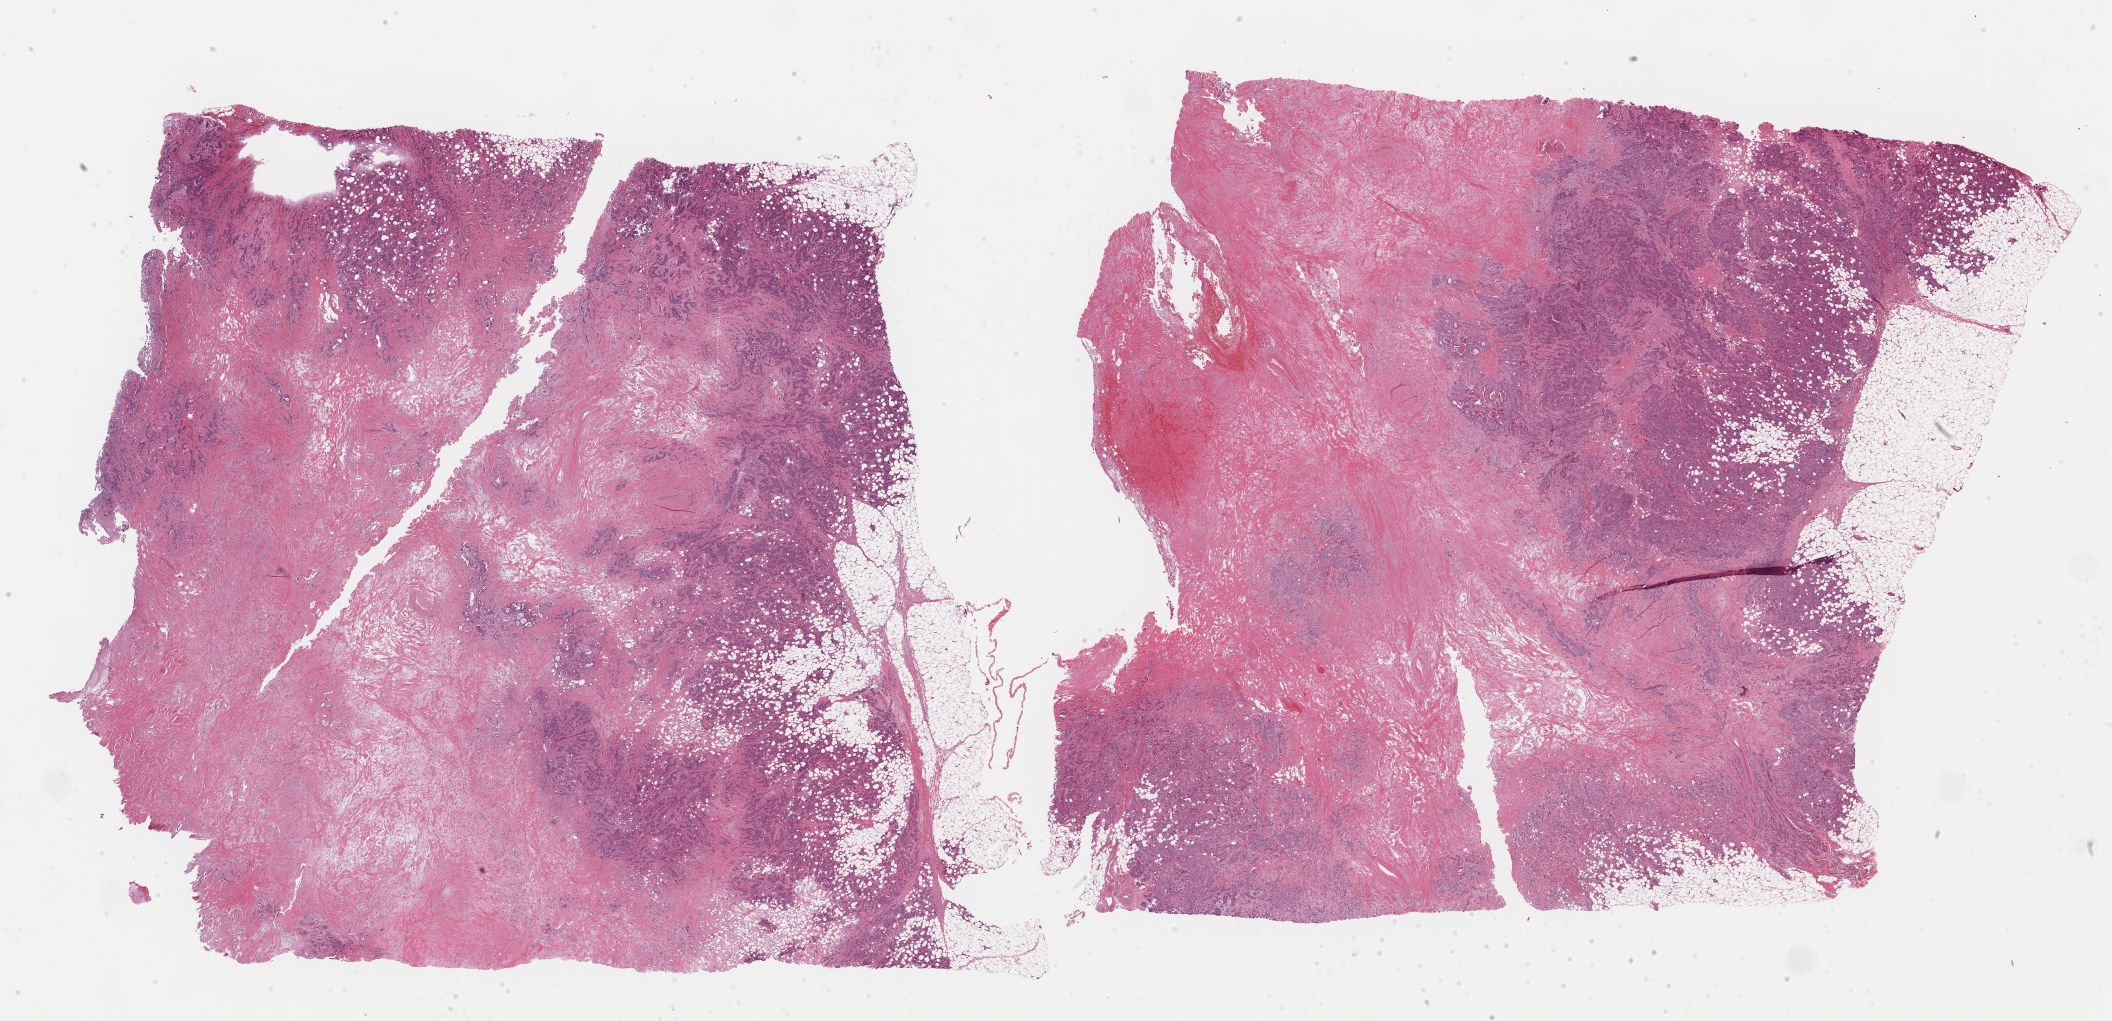
H&E whole-slide image — shown as a low-resolution overview of the whole scanned area (about 33.4 x 16.1 mm, slide scanned at 40x), formalin-fixed paraffin-embedded (FFPE) diagnostic section, sample: primary tumour, breast. Patient: female, age at initial diagnosis 54 years.
• lymph nodes positive (case pathology): 1 of 17 examined
• pathologic diagnosis: Infiltrating duct carcinoma, NOS
• AJCC pathologic stage: IIB